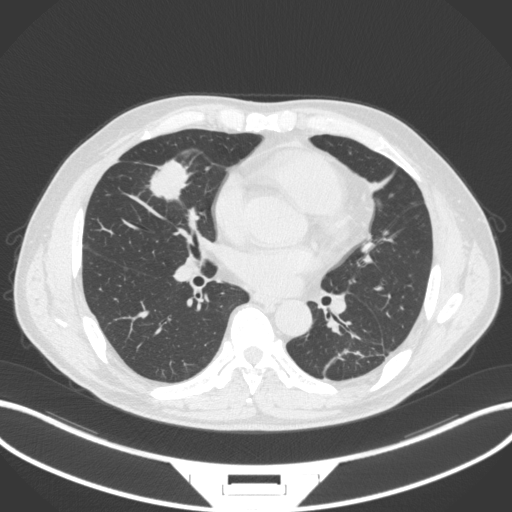
Chest CT, one axial slice; position 140 of 399 along the scan axis; reconstruction kernel B31f; 120 kVp; lung window (W 1500 / L -600 HU); 1 mm slice thickness; 512 × 512 image matrix. Patient: male, 59 years. From the clinical record (not read from this slice): clinical TNM (as recorded): T2a N1 M0.
Annotated regions visible in this slice (bounding box drawn by a radiologist):
- lung tumour (recorded histology: adenocarcinoma): bounding box <144,157,194,209> (left, top, right, bottom; pixels)